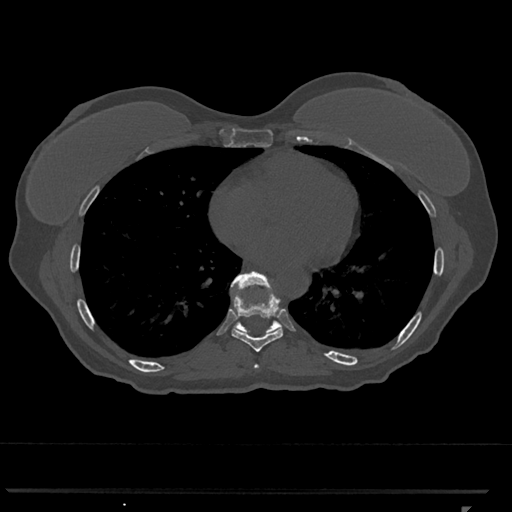
CT including the spine, one axial slice. Slice 653 of 793 in the series (ordered by position). Reconstruction kernel Br40s/3. Bone window (W 1800 / L 400 HU). 512 × 512 image matrix, field of view 380 × 380 mm. Patient: female, 62 years. From the clinical record (not read from this slice): primary cancer: renal.
Structures marked on this image (semi-automatically segmented with operator editing):
- T7 vertebra: bounding box <254,364,259,368> (left, top, right, bottom; pixels)
- T8 vertebra: <232,290,283,352>
- T9 vertebra: <231,271,282,335>